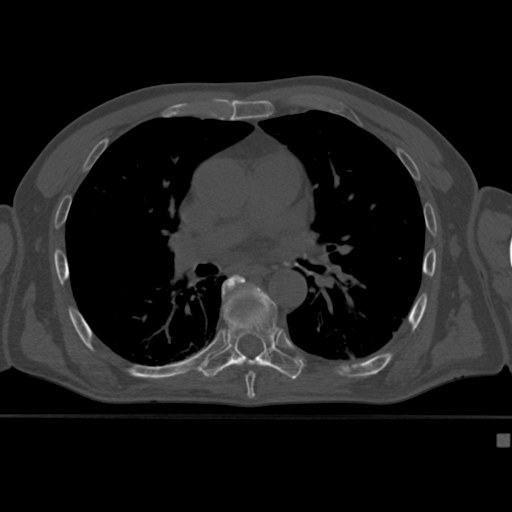
CT including the spine, one axial slice; position 269 of 430 along the scan axis; reconstruction kernel Br40s; 120 kVp; bone window (W 1800 / L 400 HU); 512 × 512 image matrix, field of view 337 × 337 mm. Male patient, age 64 years. Case-level facts recorded for this patient, not image findings: primary cancer: uterus.
Annotated regions visible in this slice (semi-automatic segmentation, software-assisted and operator-edited):
- T7 vertebra: bounding box [x1, y1, x2, y2] px = [237, 277, 256, 382]
- T8 vertebra: [202, 274, 304, 382]